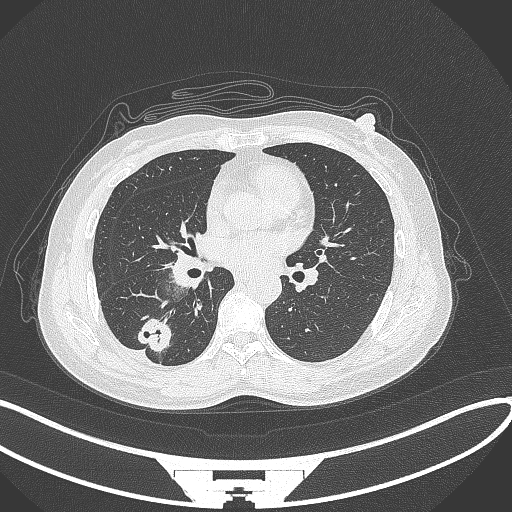
Chest CT, one axial slice; 120 kVp; lung window (W 1500 / L -600 HU); 1 mm slice thickness; 512 × 512 image matrix, field of view 400 × 400 mm. Female patient, age 55 years. Case-level facts recorded for this patient, not image findings: clinical TNM (as recorded): T1c N1 M0.
Annotated regions visible in this slice (bounding box drawn by a radiologist):
- lung tumour (recorded histology: adenocarcinoma): box from (x=133, y=313) to (x=173, y=359) px